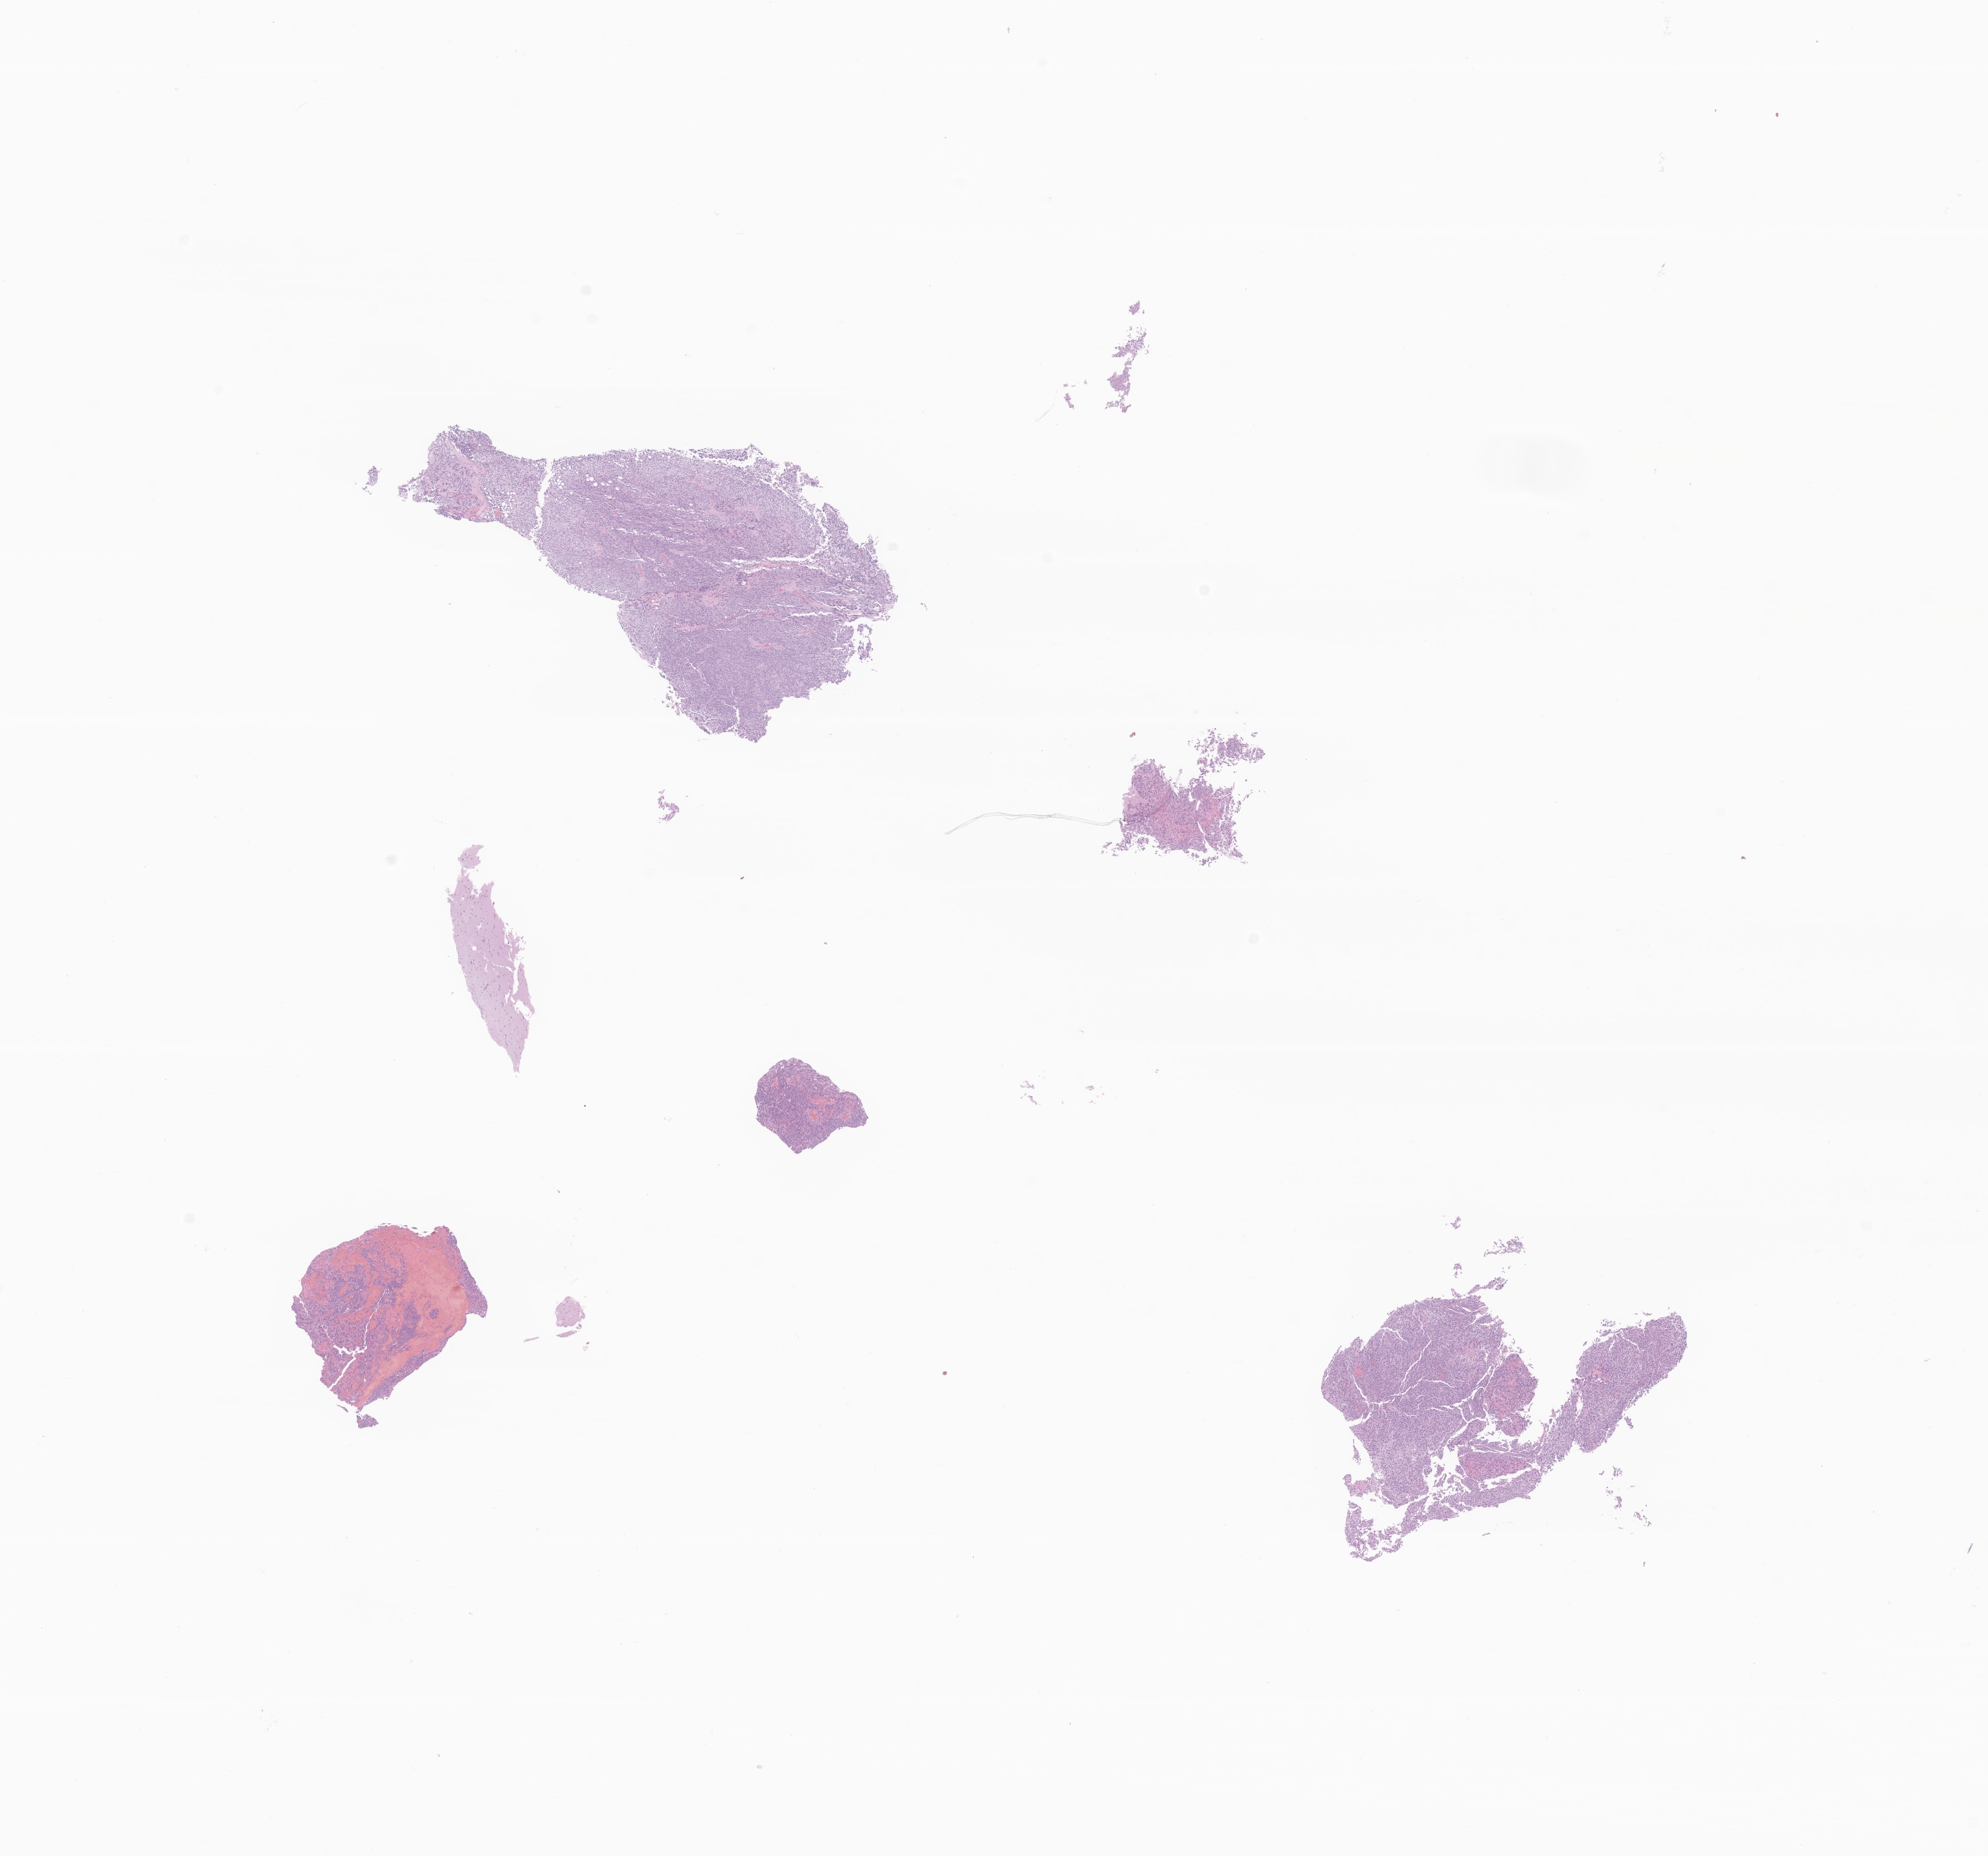
Whole-slide image, H&E stain of tumor tissue from the brain, low-resolution overview of the scanned area, about 13.0 x 12.1 mm, FFPE section. Patient female; age 199 months (16 years 7 months).
- recorded diagnosis: Neoplasm, malignant